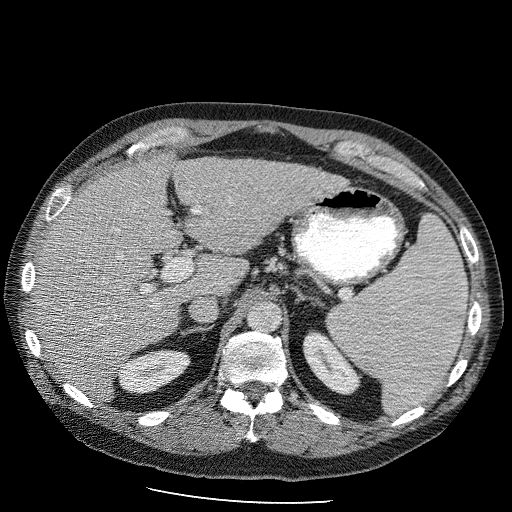
Contrast-enhanced abdominal CT (liver protocol), one axial slice. Position 62 of 98 along the scan axis. Reconstruction kernel STANDARD. 120 kVp. Soft-tissue window (W 400 / L 40 HU). 2.5 mm slice thickness. 512 × 512 image matrix, field of view 400 × 400 mm. From the clinical record (not read from this slice): diagnosis: hepatocellular carcinoma (patient treated with transarterial chemoembolisation; whether this scan precedes or follows treatment is not stated here); TNM stage (as recorded): Stage-II; Child-Pugh class: B; tumour nodularity: uninodular.
Outlined on this slice (semi-automatically segmented with operator editing):
- liver parenchyma outside the tumour (the mass and vessels are separate outlines, so this box may not span the whole liver): bounding box [x1, y1, x2, y2] px = [32, 153, 344, 402]
- liver vessels: [130, 202, 207, 330]